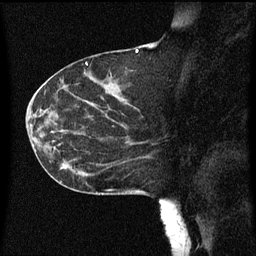
Breast MRI (dynamic contrast-enhanced), one sagittal slice. Slice 28 of 60 in the series (ordered by position). Dynamic contrast-enhanced series, image 2 of 3 at this slice position (ordered by acquisition). 1.5 T. TE 4.2 ms, TR 8 ms. 2 mm slice thickness. 256 × 256 image matrix, field of view 200 × 200 mm. Patient: female, 55 years.
Structures marked on this image (semi-automatic segmentation, software-assisted and operator-edited):
- analysis volume of interest (the breast-tissue region the enhancement analysis was run in; not a lesion): bounding box (x1, y1, x2, y2) in pixels: (46, 124, 151, 183)
- tumour enhancement mask (voxels above the 70 % enhancement threshold inside the analysis volume of interest): (50, 142, 147, 169)